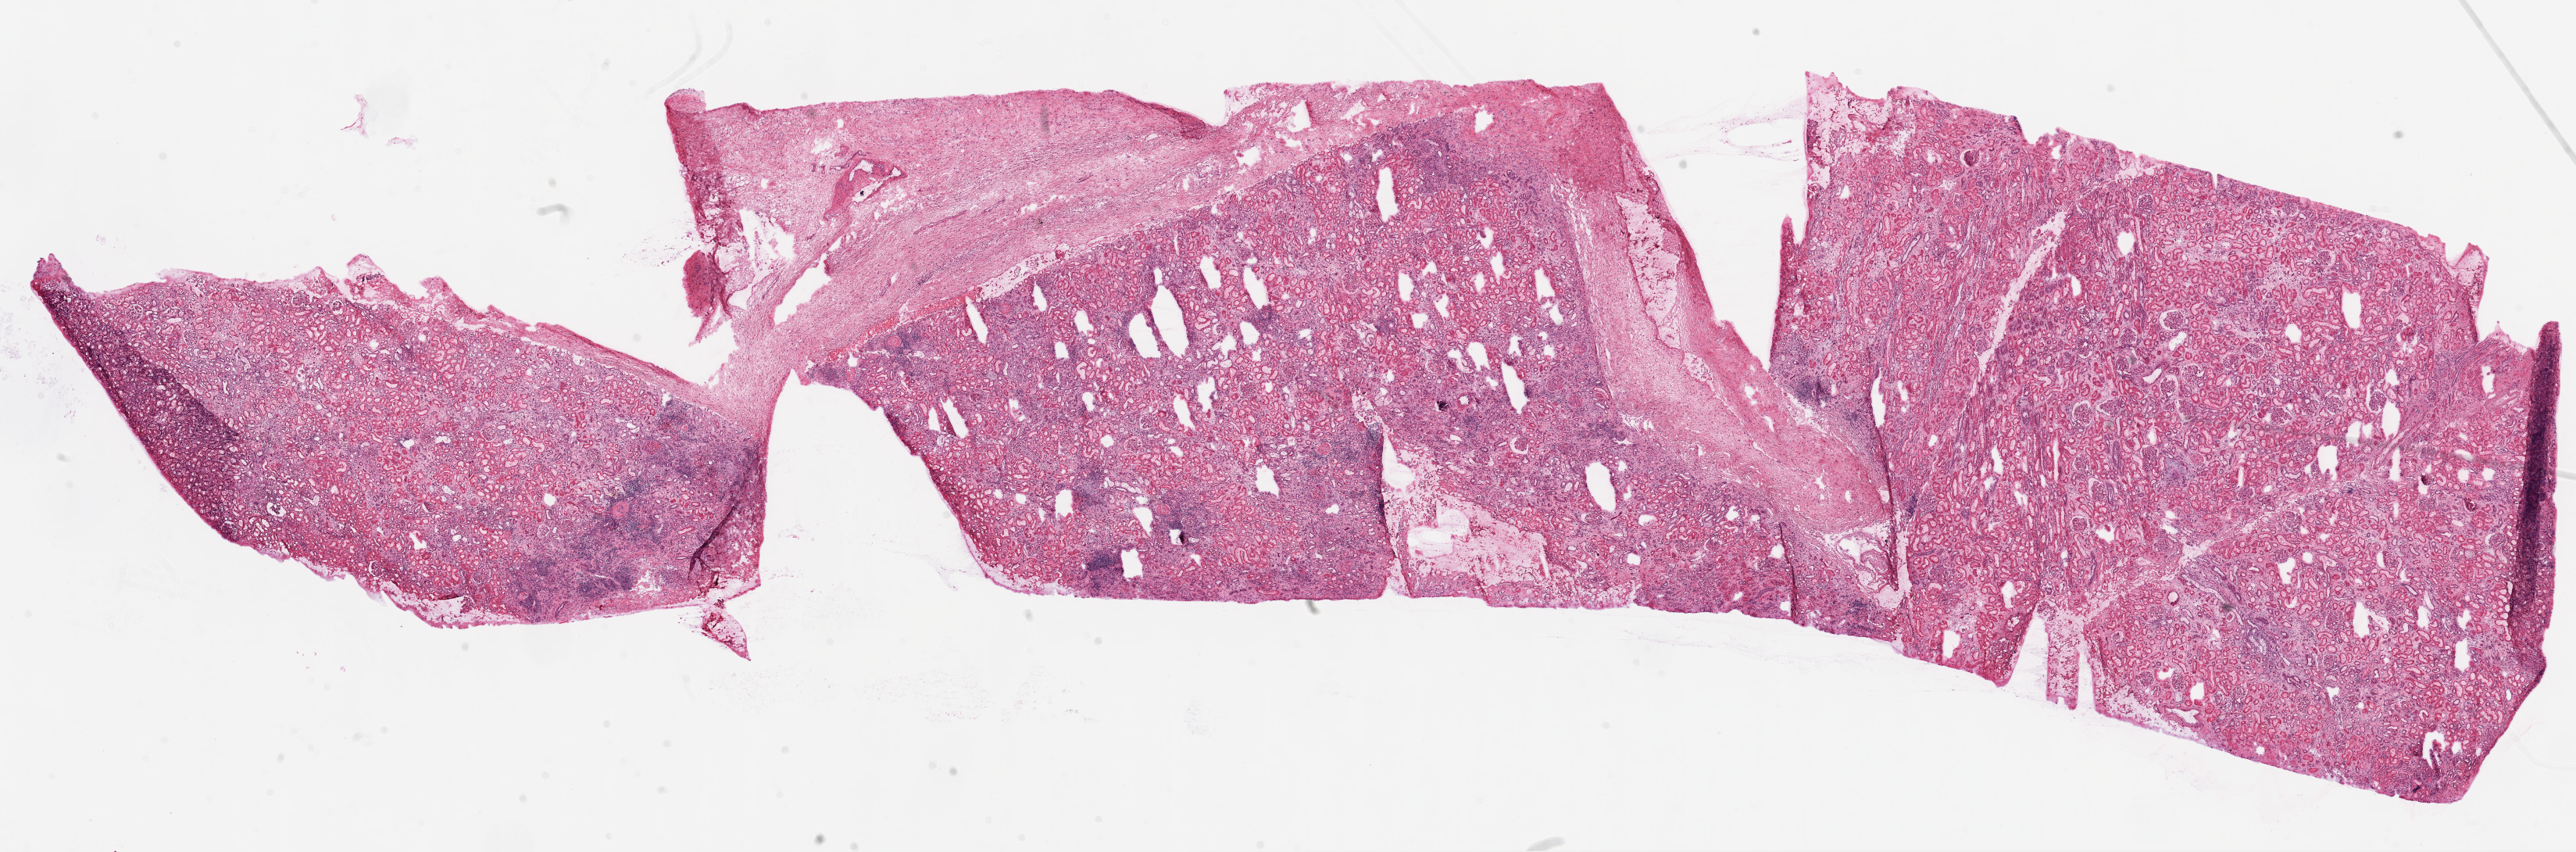
Whole-slide histology image, H&E, shown as a low-resolution overview of the whole scanned area (about 26.6 x 8.8 mm), frozen section from the top of the tissue portion, sample: solid tissue normal (non-tumour tissue), kidney. Male patient; age at initial diagnosis 73 years.
This section: solid tissue normal (non-tumour) sample from the same patient. Patient diagnosis: Clear cell adenocarcinoma, NOS.